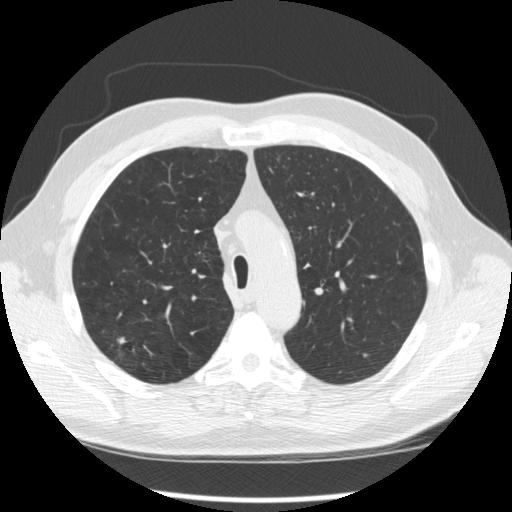
Axial slice from a low-dose chest CT screening exam; second screening round (one year after baseline); lung window (W 1500 / L -600 HU); 2.5 mm slice thickness; standard (soft-tissue) reconstruction kernel (STANDARD); 120 kVp; slice 76 of 289 in the series; 512 × 512 image matrix. Male participant, aged 64 years at enrolment.
Lesion marked by an expert reader, bounding box <107,323,151,365> (left, top, right, bottom; pixels). The screening reader recorded 3 non-calcified nodules or masses ≥4 mm on this exam (right upper lobe, right upper lobe, right upper lobe); which of them this box marks is not recorded. Participant outcome: lung cancer diagnosed 411 days after this screen (after the third annual screen) — adenocarcinoma, NOS, right upper lobe, moderately differentiated (G2), stage IA (AJCC 6th edition), 14 mm at pathology.